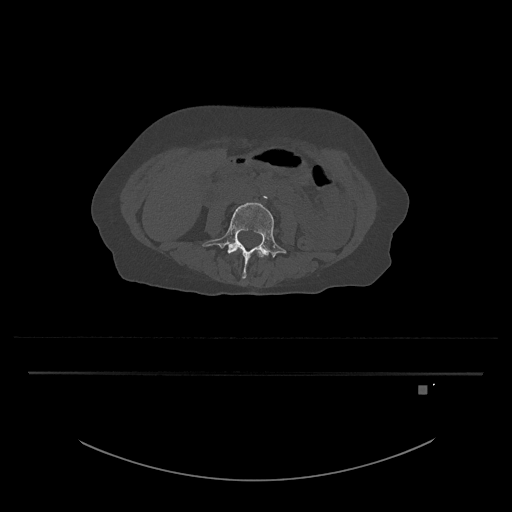
CT including the spine, one axial slice. 120 kVp. Bone window (W 1800 / L 400 HU). 0.5 mm slice thickness. 512 × 512 image matrix. Female patient, age 57 years. From the clinical record (not read from this slice): primary cancer: cervical.
Outlined on this slice (semi-automatically segmented with operator editing):
- L3 vertebra: bounding box <257,251,264,257> (left, top, right, bottom; pixels)
- L4 vertebra: <202,202,287,278>